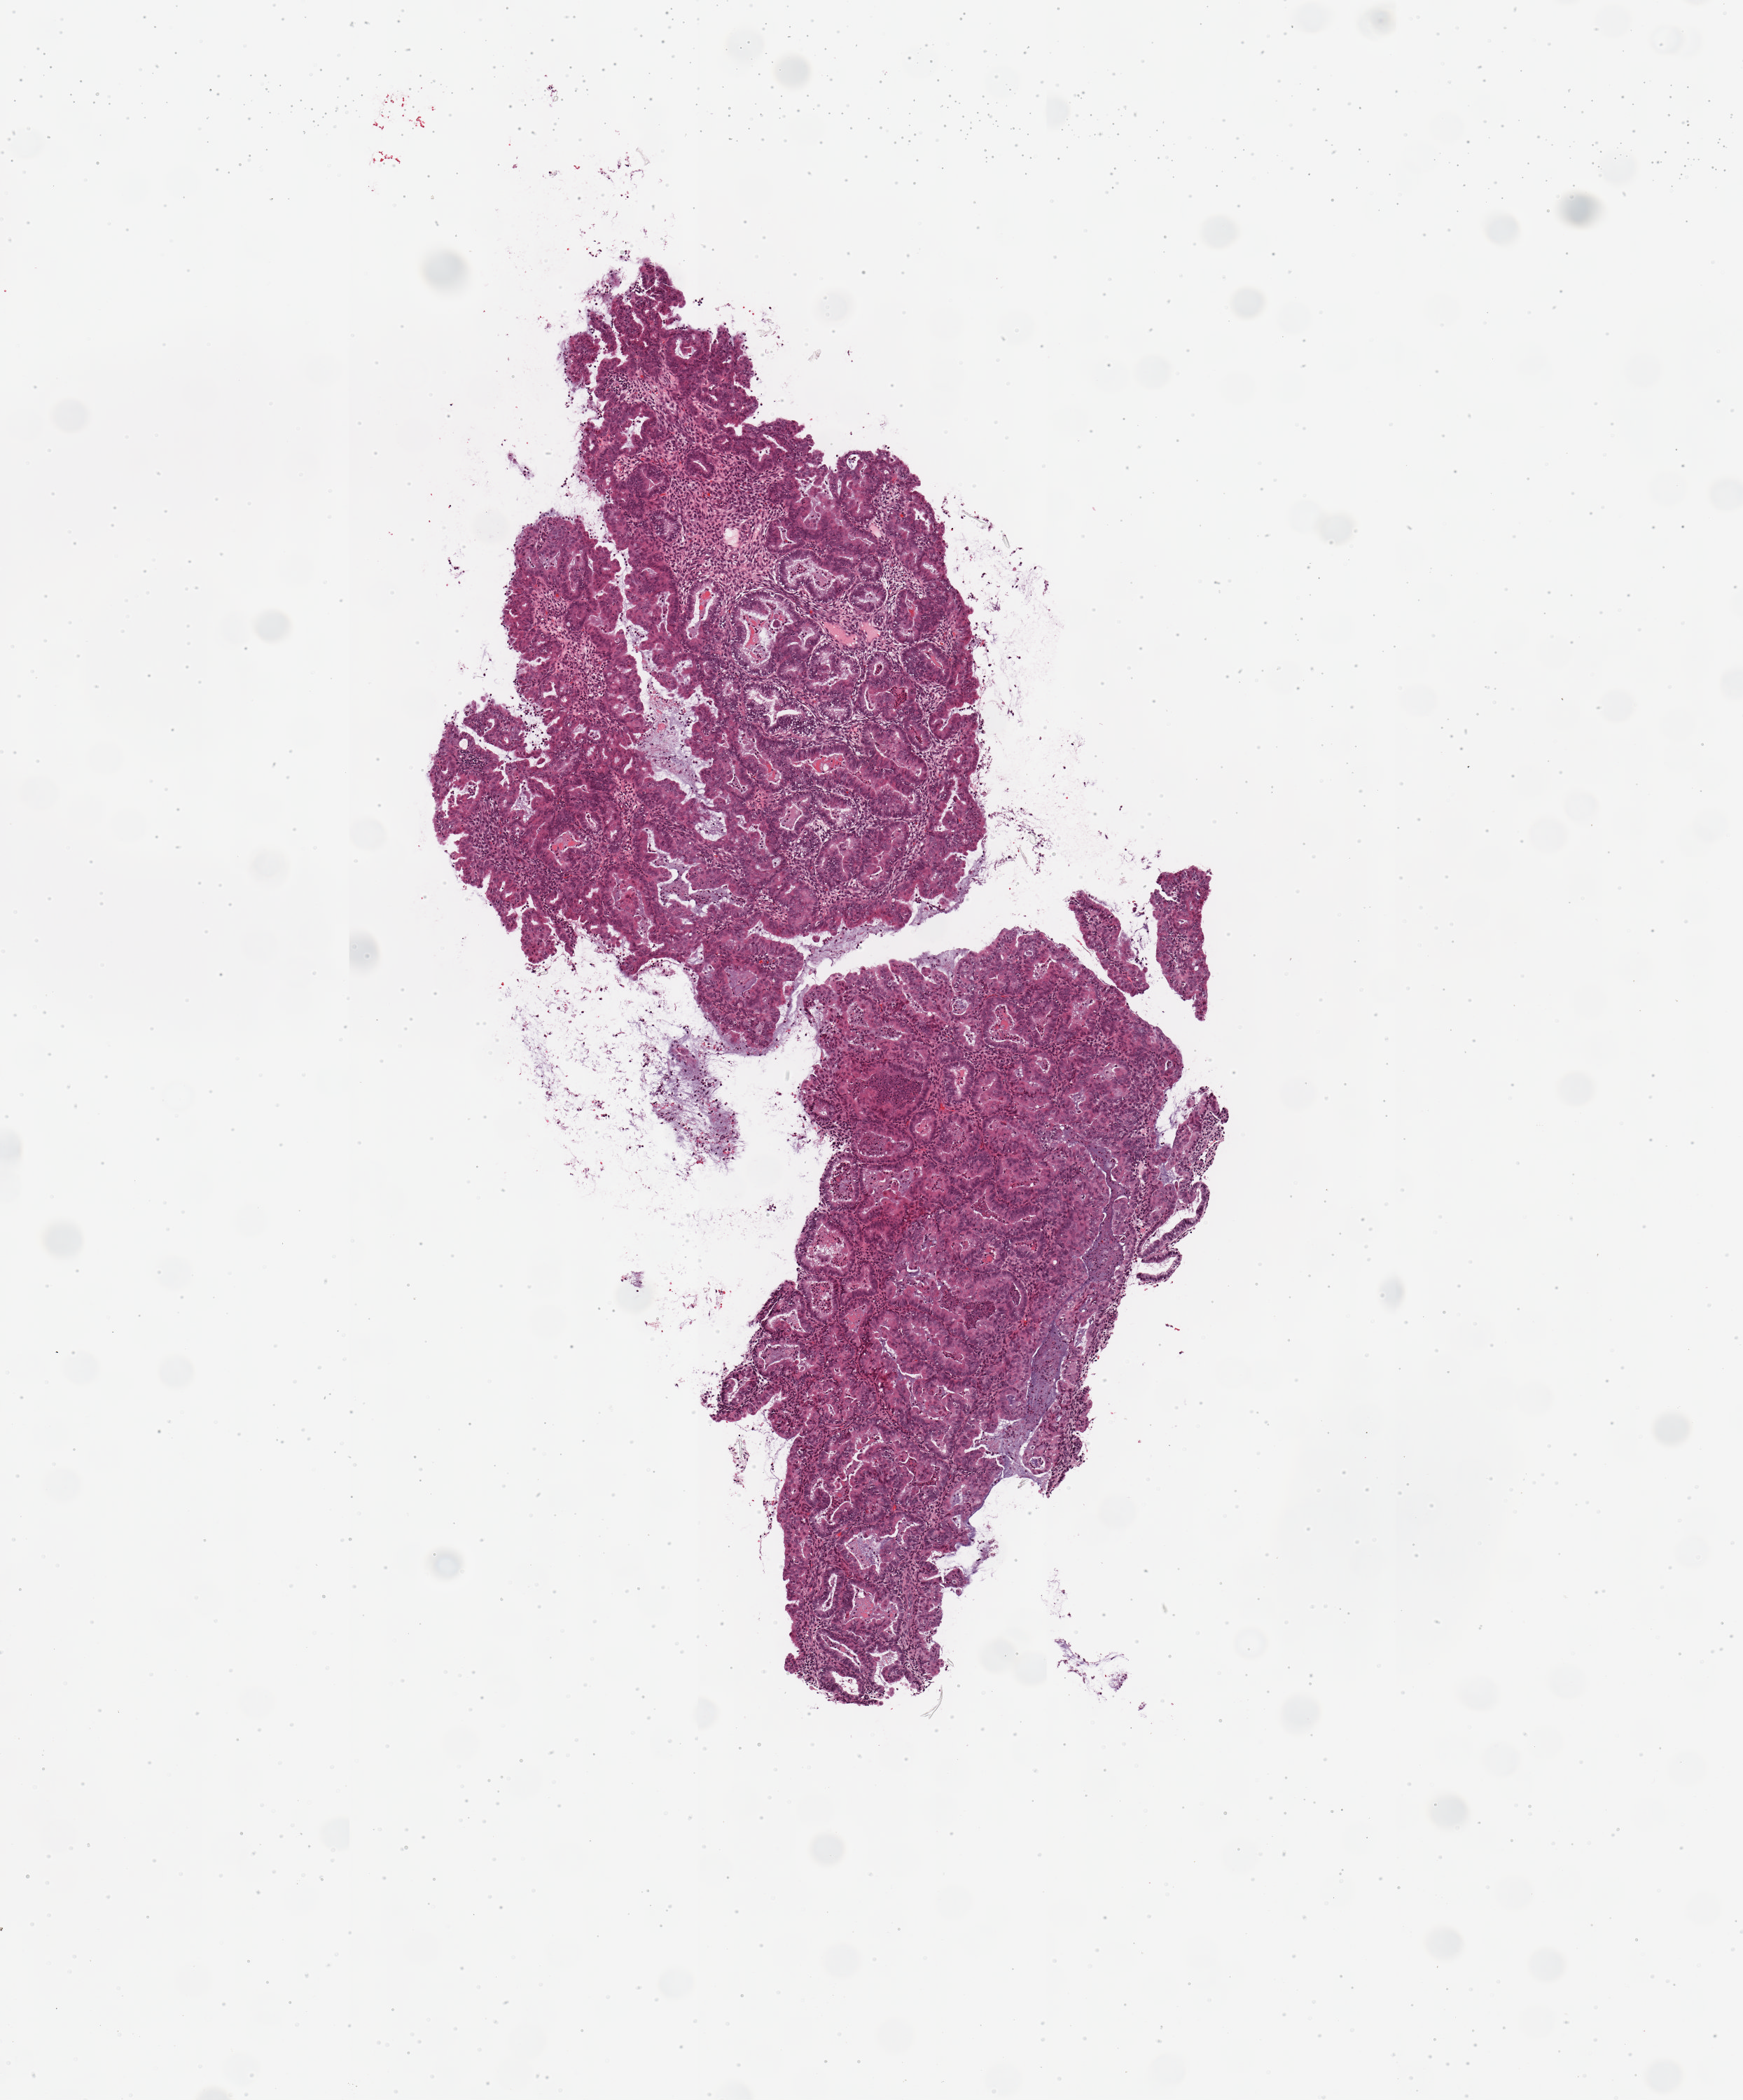
Whole-slide histology image, H&E, whole scanned area (about 4.9 x 5.9 mm, slide scanned at 20x) shown as a low-resolution overview; tumour tissue sample, uterus. Female, 49 y/o.
* patient diagnosis (cohort enrolment): corpus endometrial carcinoma (uterus)